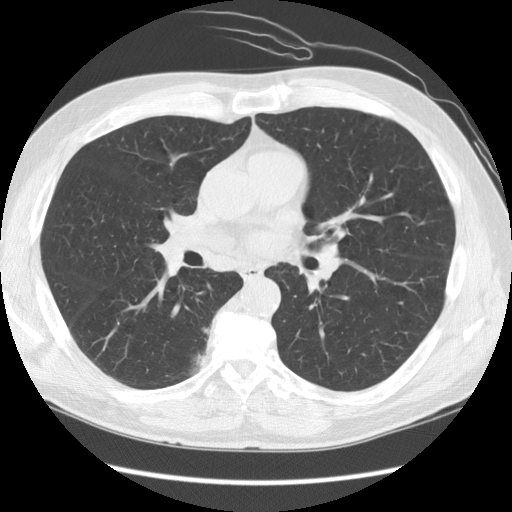
Chest CT (low-dose screening protocol), one axial image; baseline annual screen; lung window (W 1500 / L -600 HU); 2.5 mm slice thickness. Male, age 69 years at enrolment.
Expert-annotated lung lesion, bounding box [x1, y1, x2, y2] px = [159, 314, 226, 377]. No non-calcified nodule or mass ≥4 mm was recorded by the screening reader at this exam. Participant outcome: lung cancer diagnosed 497 days after this screen — bronchiolo-alveolar adenocarcinoma, NOS, right lower lobe, well differentiated (G1), stage IB (AJCC 6th edition), 23 mm at pathology.